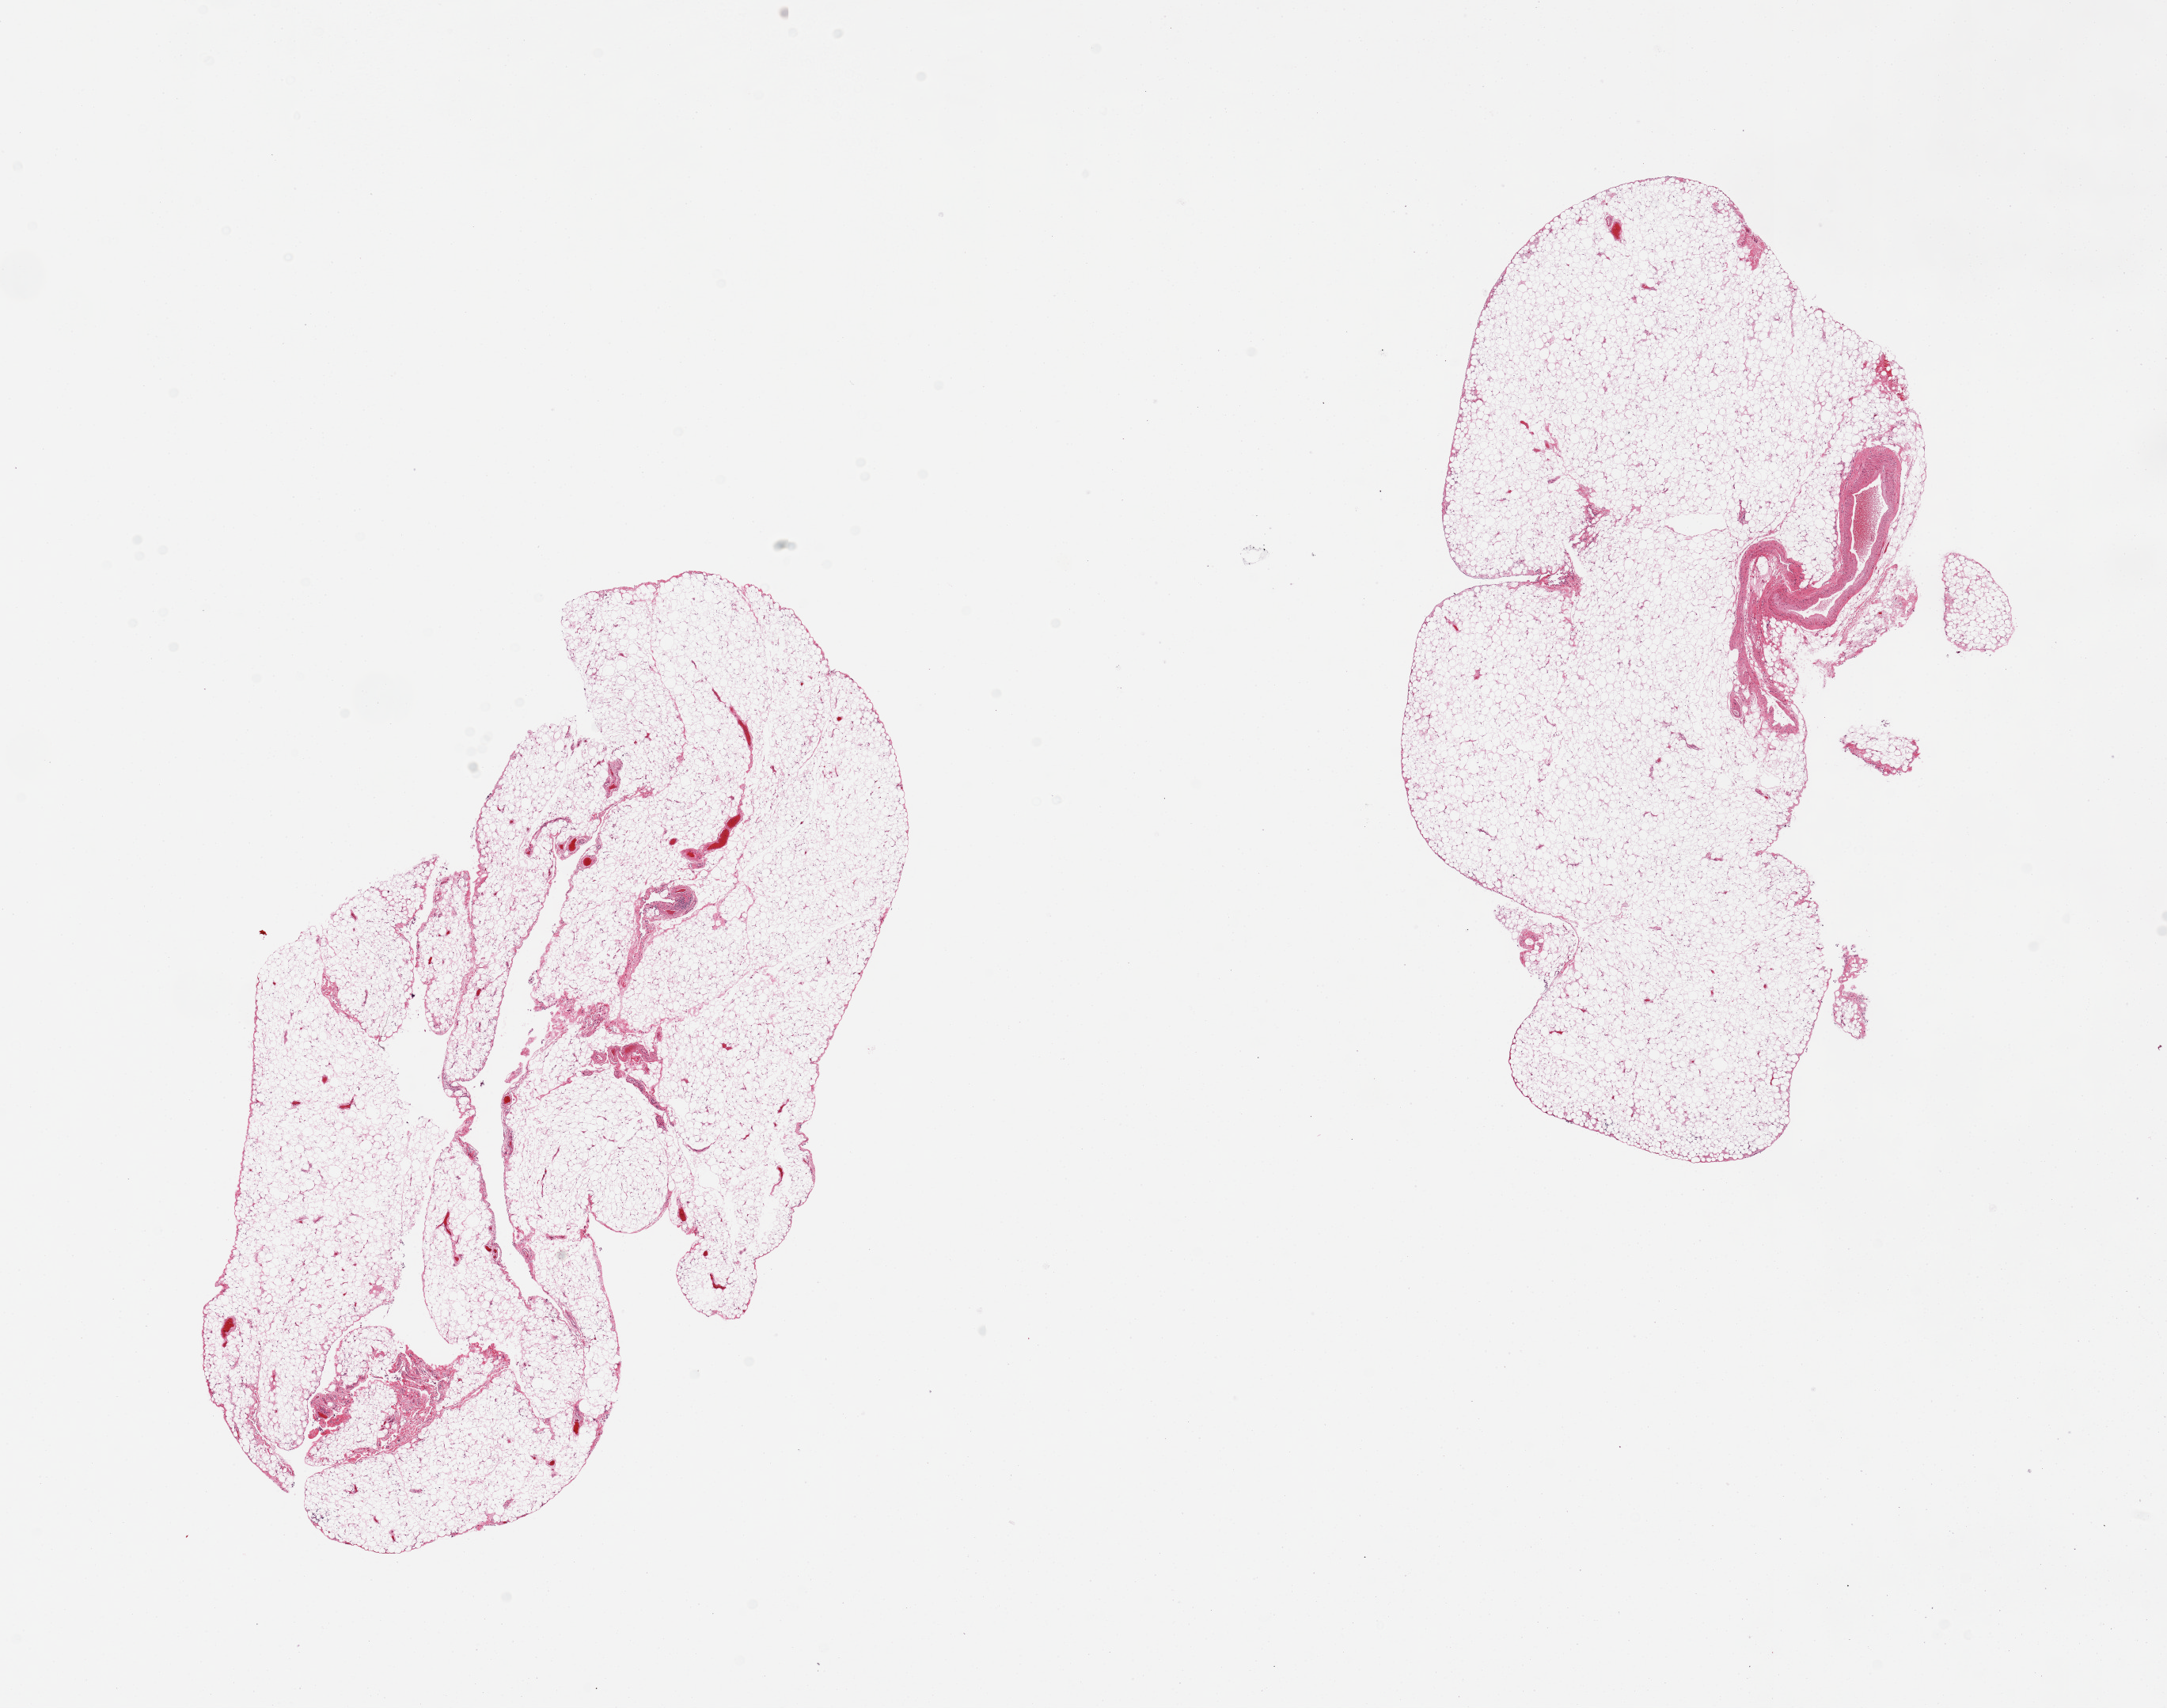
Digitized H&E-stained section — low-resolution overview of the scanned area, about 21.7 x 17.1 mm (from a 20x scan); PAXgene-fixed paraffin-embedded (PFPE) section; sampled site (target tissue): omentum; donor tissue sample. Donor sex: female.
Reviewer comment on this tissue sample: 2 pieces.